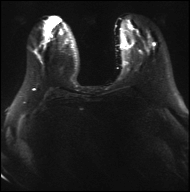
Breast MRI, one axial slice; diffusion-weighted series; image 2 of 4 stored at this slice position (different b-values; order by instance number); 3 T; 4 mm slice thickness; 190 × 192 image matrix, field of view 317 × 320 mm. Female patient.
Structures marked on this image (expert manual segmentation):
- tumour on diffusion-weighted imaging: box from (x=79, y=22) to (x=87, y=26) px